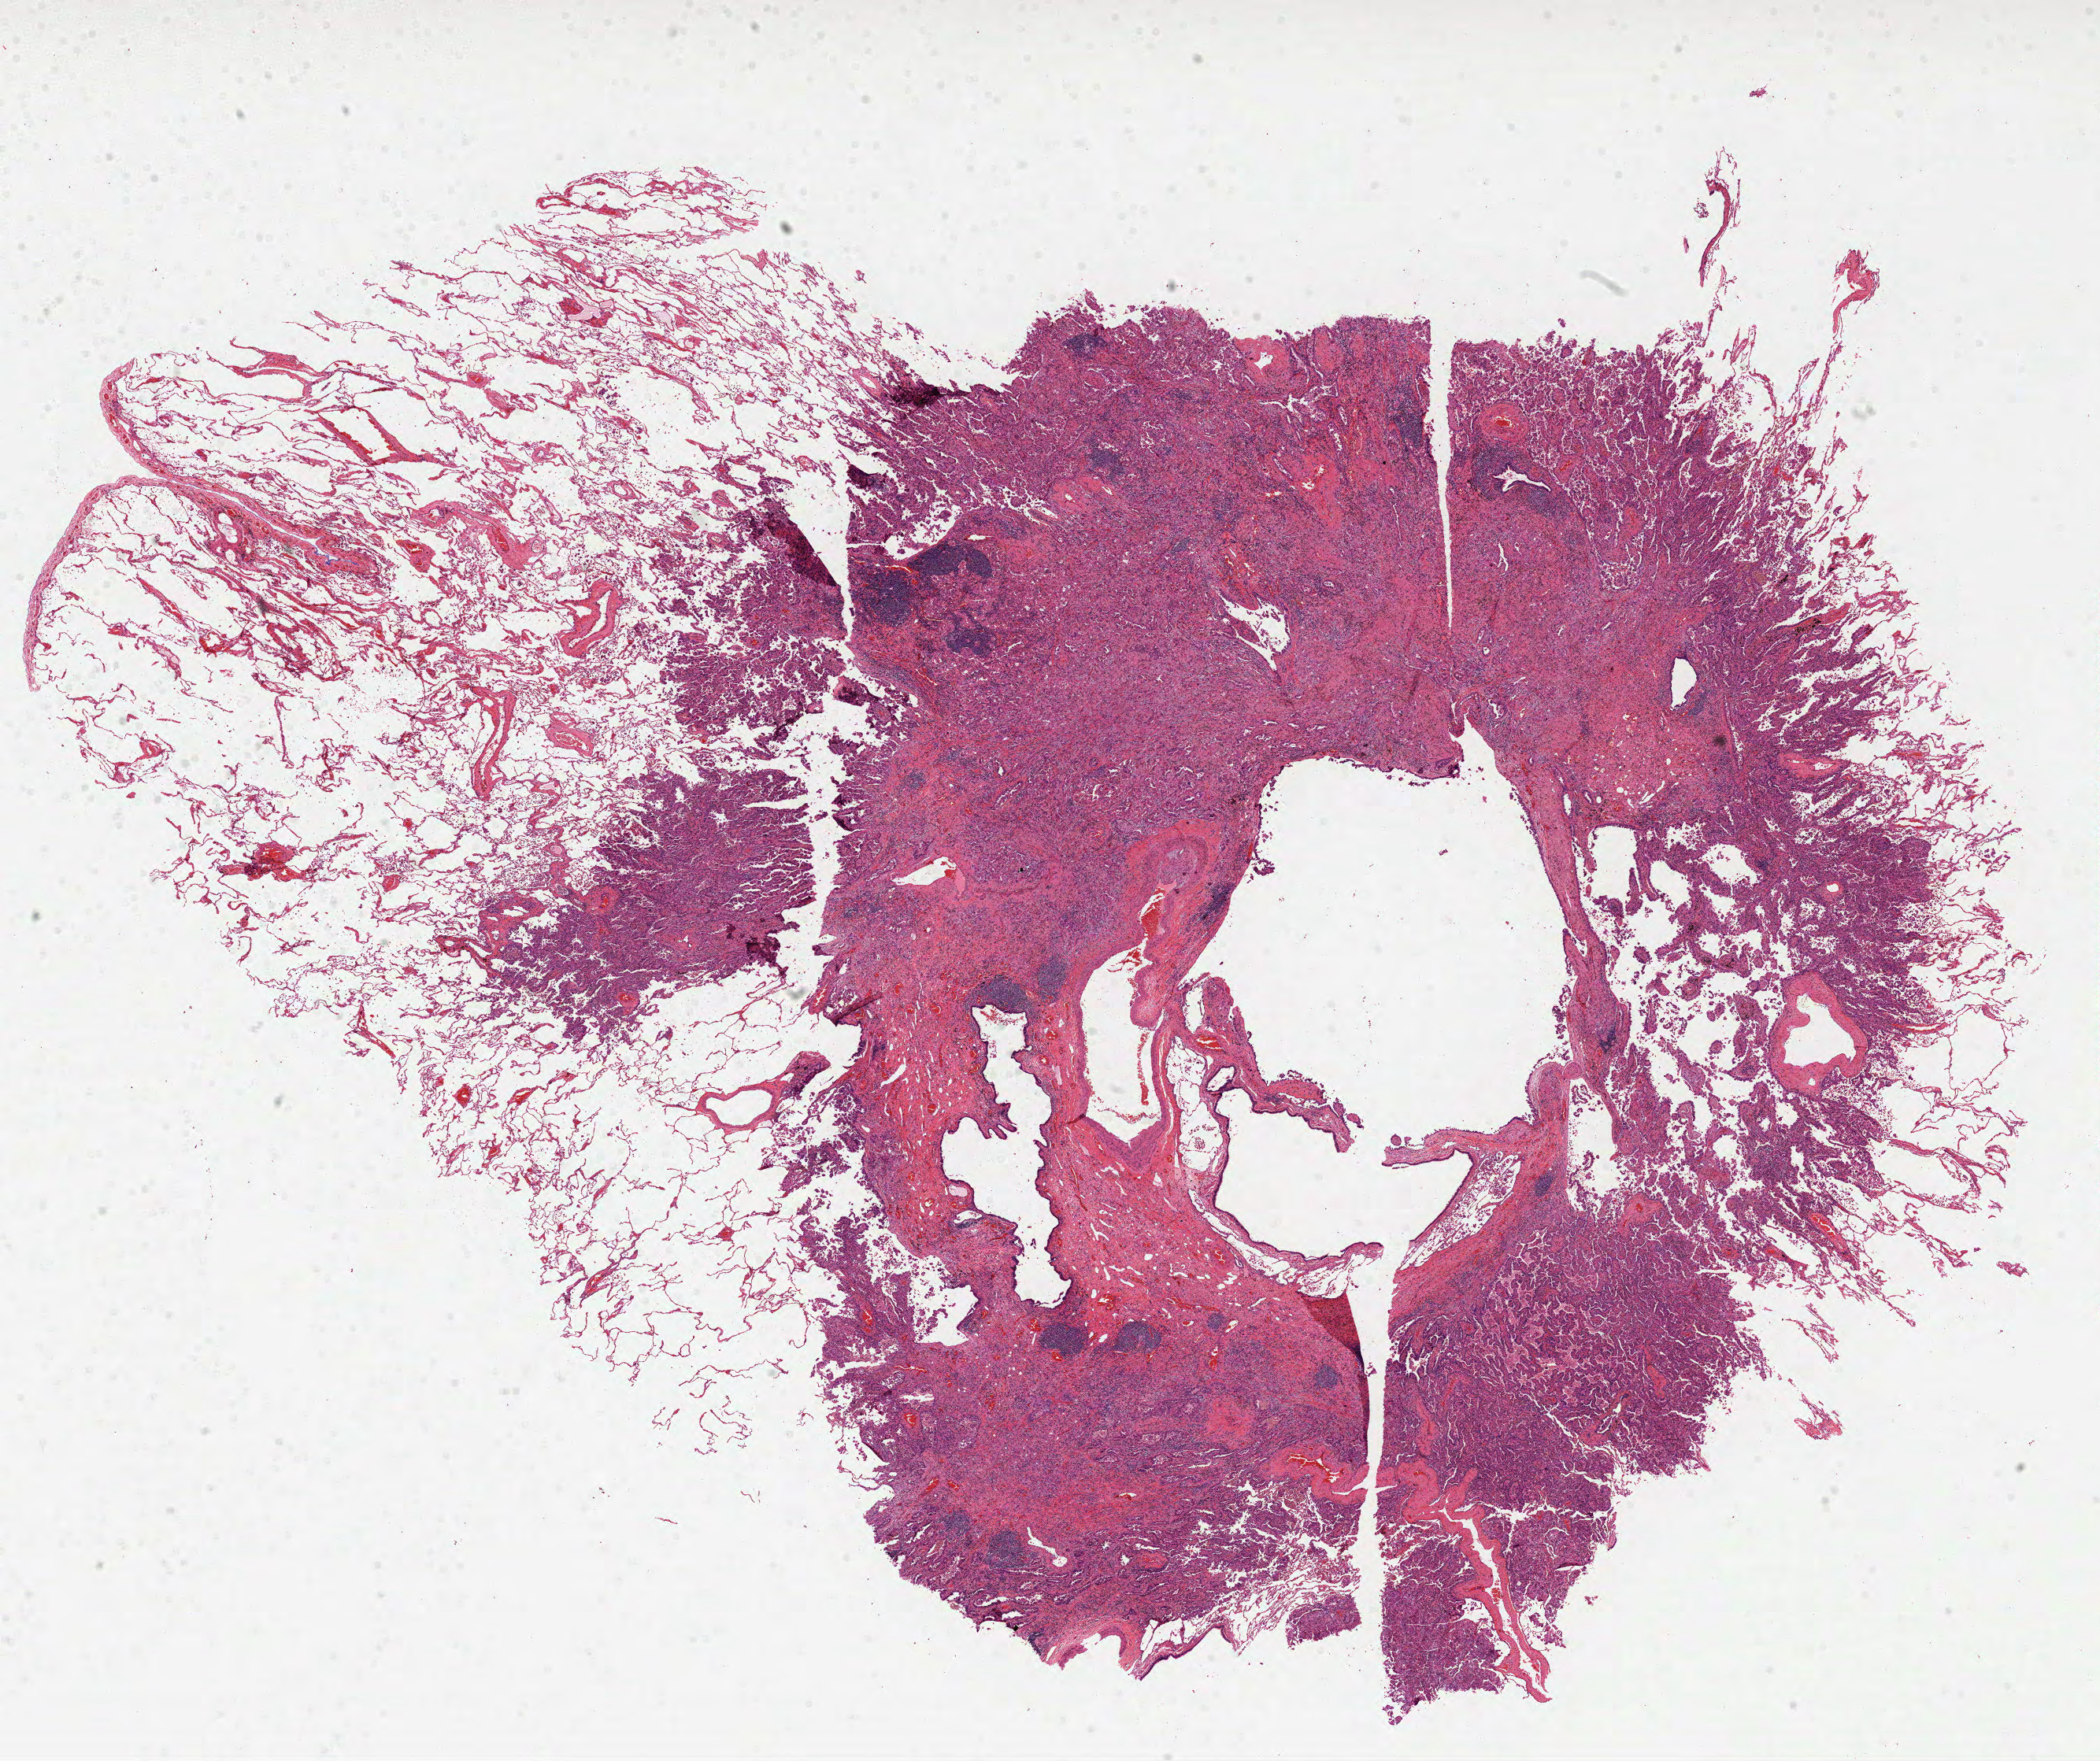
Whole-slide histology image, H&E-stained — shown as a low-resolution overview of the whole scanned area (about 21.5 x 18.0 mm, from a 40x scan), formalin-fixed paraffin-embedded (FFPE) diagnostic section, sample: primary tumour, lung. Patient: male, age at initial diagnosis 56 years.
Histologic diagnosis: Adenocarcinoma with mixed subtypes.